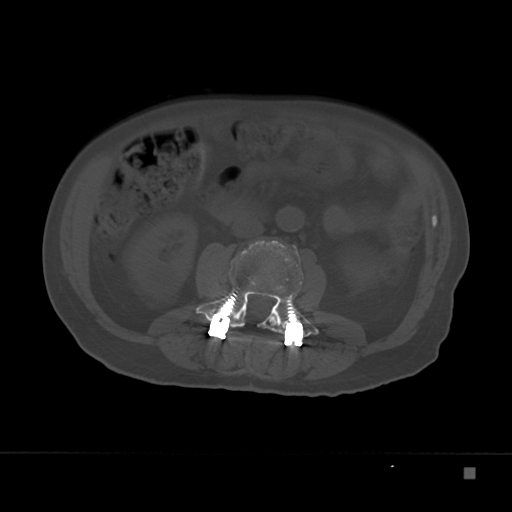
CT including the spine, one axial slice; position 73 of 332 along the scan axis; reconstruction kernel Br40s; bone window (W 1800 / L 400 HU); 1.5 mm slice thickness; 512 × 512 image matrix, field of view 389 × 389 mm. Male patient, age 72 years. Case-level facts recorded for this patient, not image findings: primary cancer: skeletal.
Annotated regions visible in this slice (semi-automatically segmented with operator editing):
- L2 vertebra: bounding box <268,316,277,326> (left, top, right, bottom; pixels)
- L3 vertebra: <195,239,318,338>